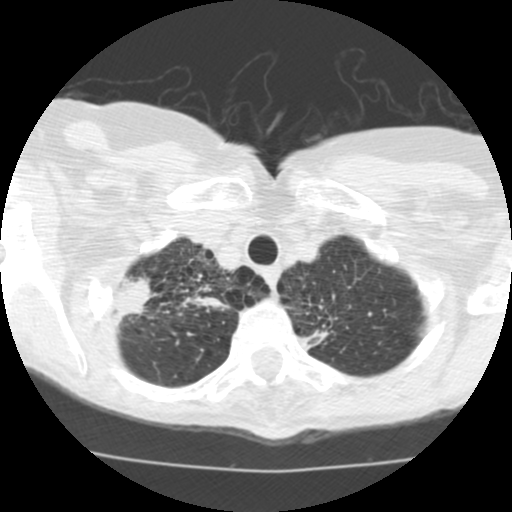
Low-dose screening chest CT, axial slice, second annual screen, lung window (W 1500 / L -600 HU), 2.5 mm slice thickness. Female participant, aged 68 years at enrolment. Current smoker at enrolment.
- Expert-annotated lung lesion, bounding box [x1, y1, x2, y2] px = [102, 264, 163, 334].
- The screening reader recorded 3 non-calcified nodules or masses ≥4 mm on this exam (right upper lobe, right upper lobe, right middle lobe); which of them this box marks is not recorded.
- Later outcome: lung cancer diagnosed 36 days after this screen — large cell neuroendocrine carcinoma, right upper lobe, undifferentiated (G4), stage IB (AJCC 6th edition), 22 mm at pathology.